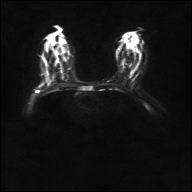
Breast MRI, one axial slice; slice 18 of 36 in the series (ordered by position); diffusion-weighted series; image 2 of 4 stored at this slice position (different b-values; order by instance number); 1.5 T; 192 × 192 image matrix, field of view 360 × 360 mm. Female patient.
Annotated regions visible in this slice (expert manual segmentation):
- tumour on diffusion-weighted imaging: box from (x=39, y=83) to (x=44, y=87) px